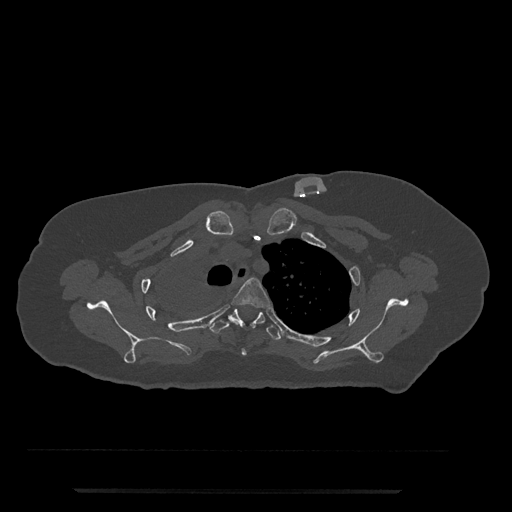
CT including the spine, one axial slice. Position 612 of 797 along the scan axis. Reconstruction kernel Br40s/3. 120 kVp. Bone window (W 1800 / L 400 HU). 0.5 mm slice thickness. 512 × 512 image matrix. Female patient, age 51 years. From the clinical record (not read from this slice): primary cancer: neuro.
Structures marked on this image (semi-automatically segmented with operator editing):
- T3 vertebra: box from (x=231, y=278) to (x=270, y=356) px
- T4 vertebra: (x=209, y=309)–(x=281, y=341)